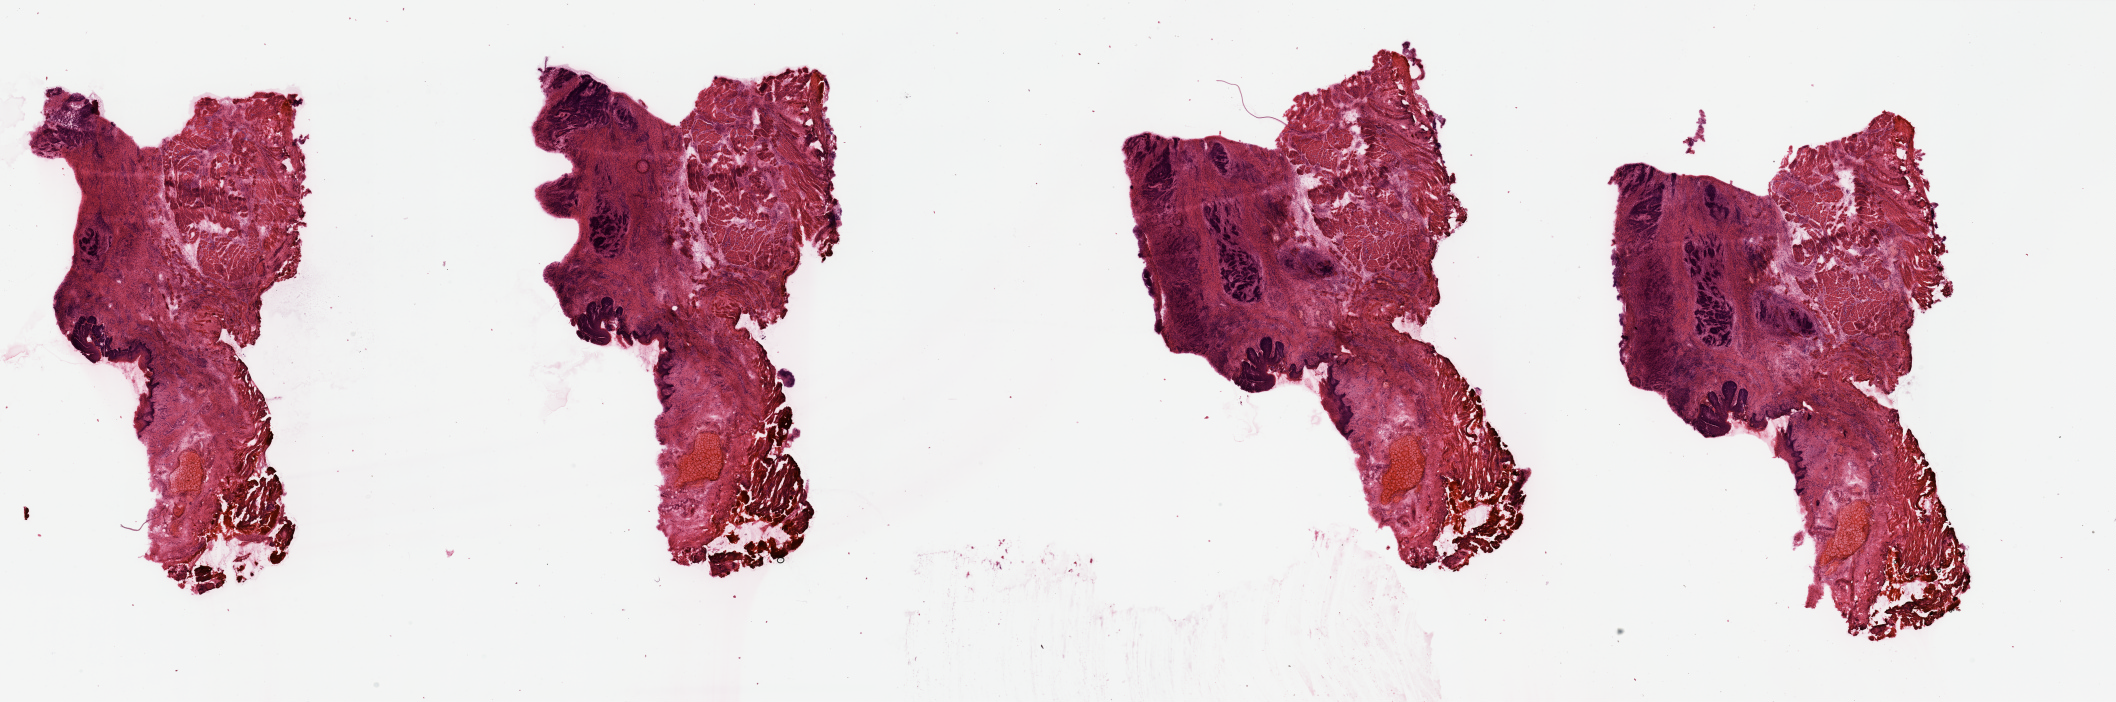
Whole-slide histology image, H&E-stained, whole scanned area (about 33.5 x 11.1 mm, acquisition: 20x scan) shown as a low-resolution overview. Head and neck, tissue type not recorded. 53-year-old male patient.
Patient diagnosis: Squamous cell carcinoma, NOS.